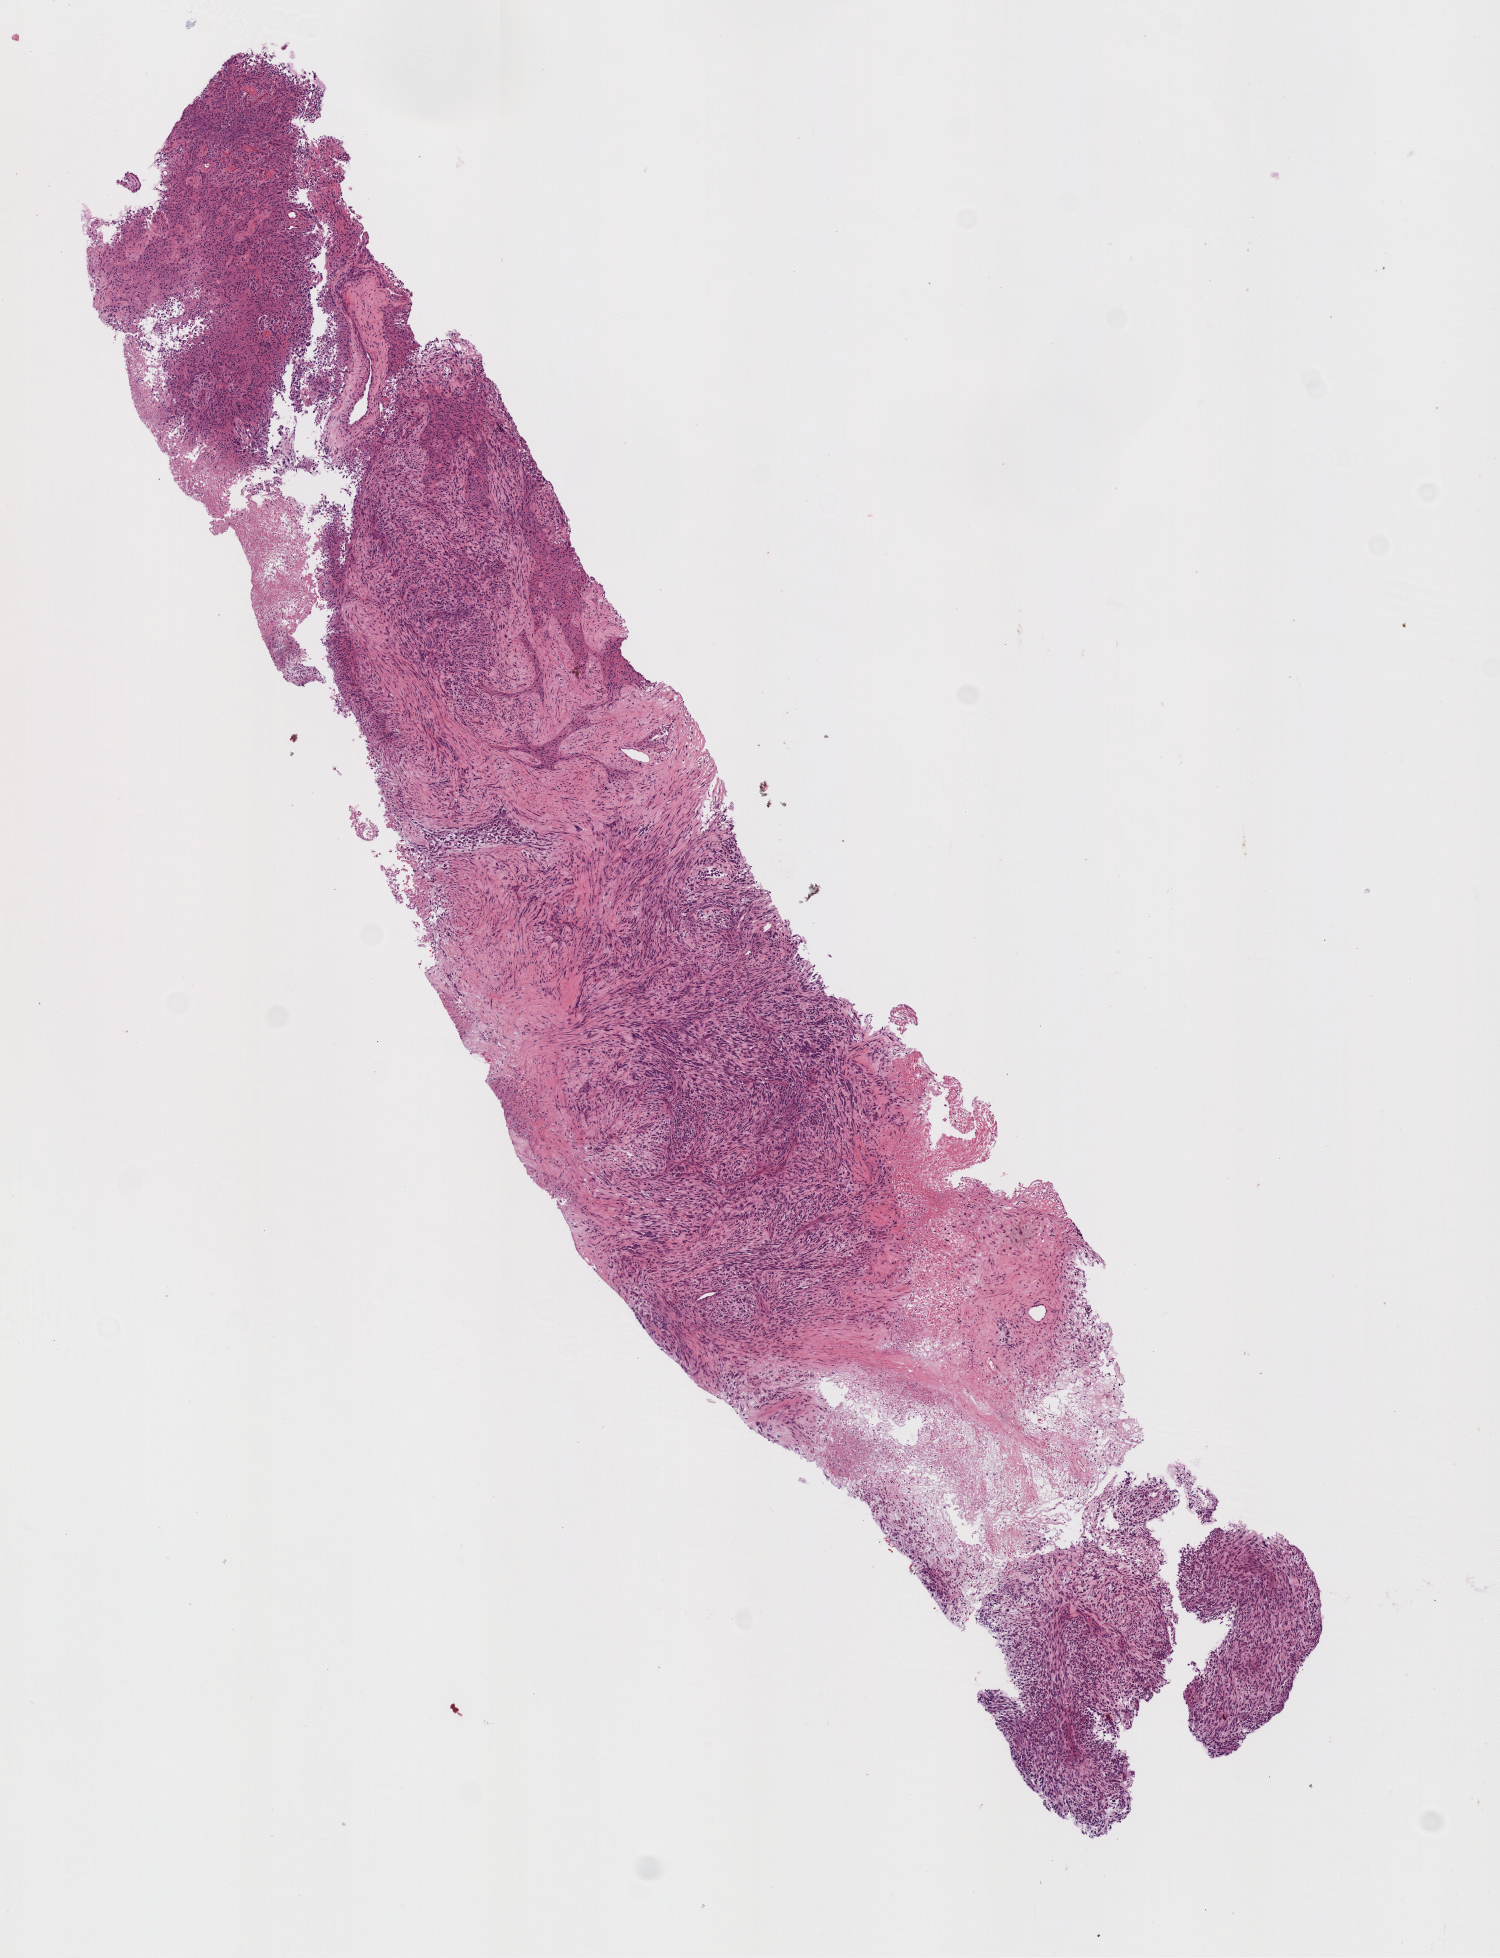
Digitized Hematoxylin and eosin (H&E) stained tissue section (whole slide) — a low-resolution overview of the entire scanned area, about 6.0 x 7.9 mm (from a 20x scan); formalin-fixed paraffin-embedded (FFPE) diagnostic section; primary tumour sample from the brain. Male patient; age at initial diagnosis 71 years.
Histologic diagnosis: Glioblastoma.